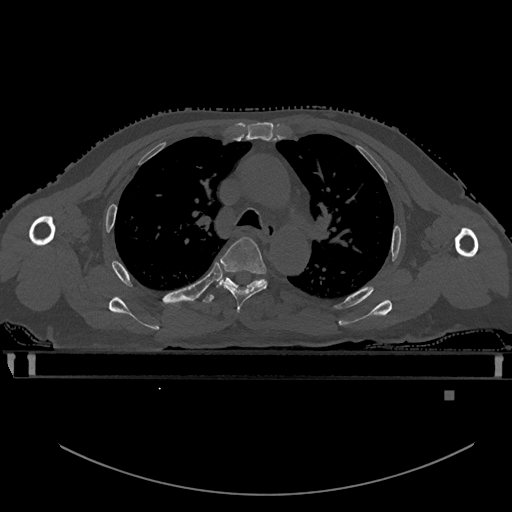
CT including the spine, one axial slice; position 391 of 969 along the scan axis; bone window (W 1800 / L 400 HU); 0.5 mm slice thickness; 512 × 512 image matrix, field of view 456 × 456 mm. Patient: male, 82 years. From the clinical record (not read from this slice): primary cancer: prostate; vertebrae with lytic lesions (as recorded): T11, T9, T8, T2.
Outlined on this slice (semi-automatically segmented with operator editing):
- T4 vertebra: bounding box (x1, y1, x2, y2) in pixels: (220, 236, 268, 312)
- T5 vertebra: (202, 271, 264, 304)